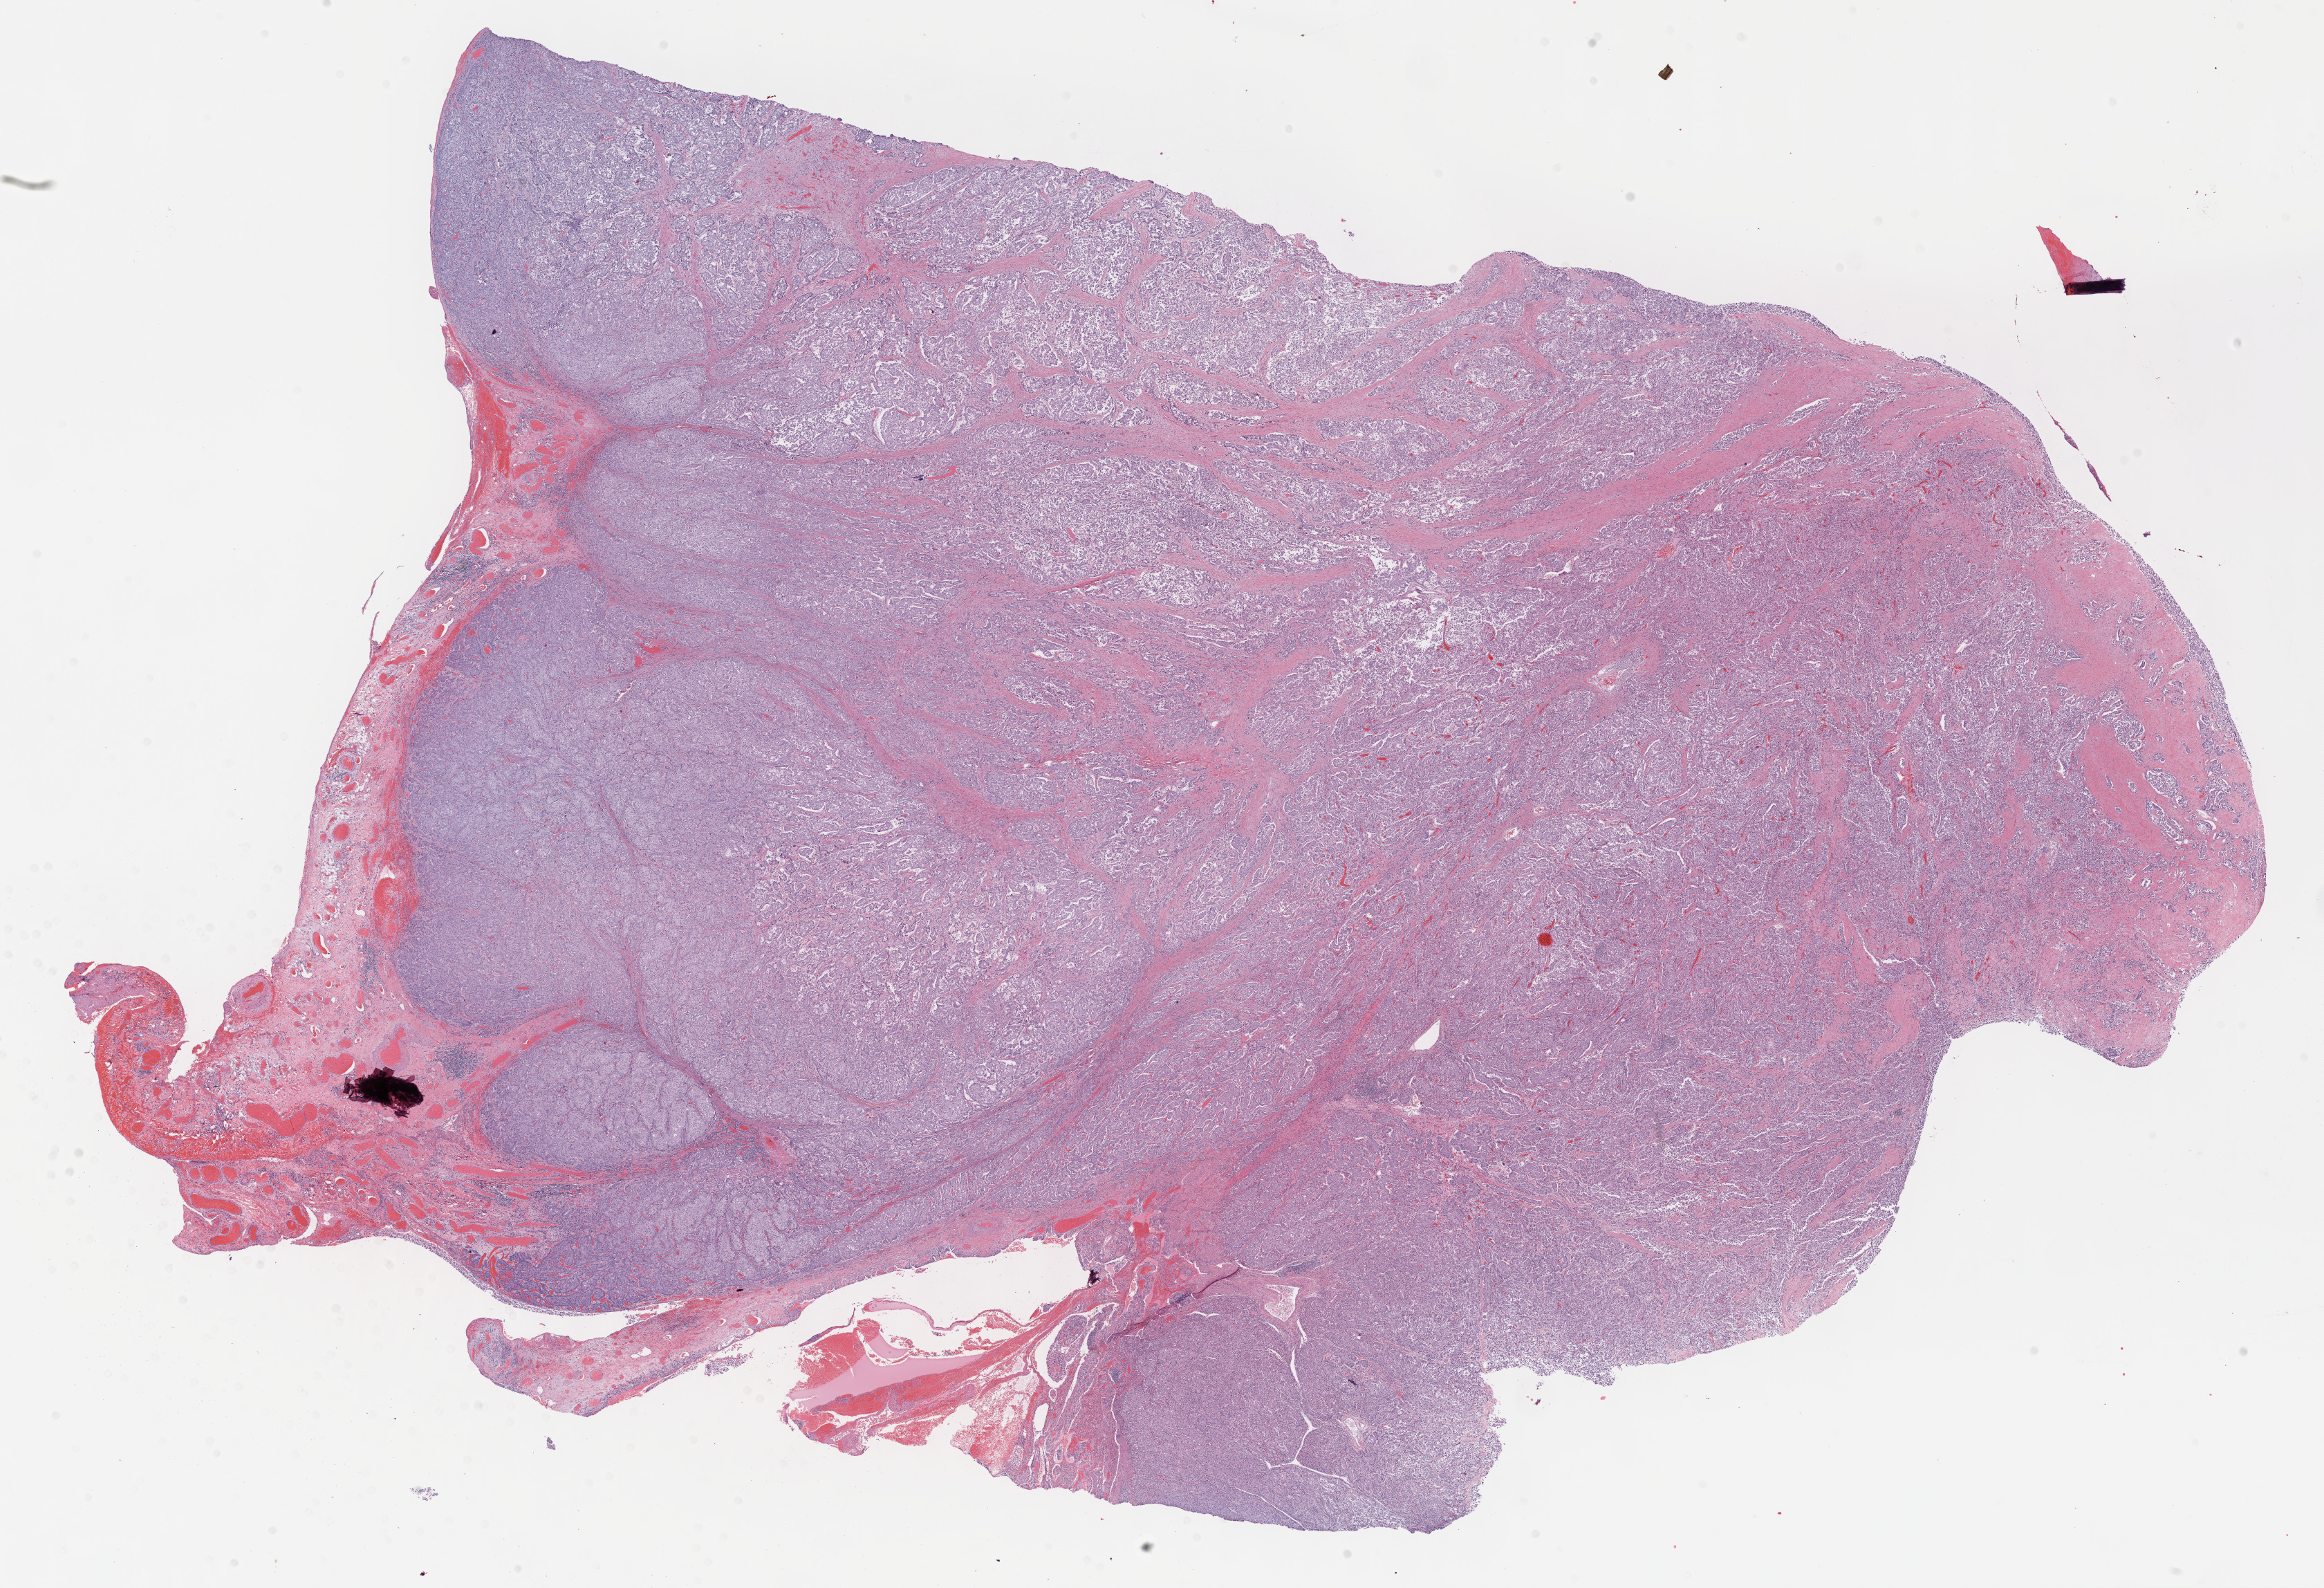
Whole-slide histology image, H&E — shown as a low-resolution overview of the whole scanned area (about 27.2 x 18.6 mm). Formalin-fixed paraffin-embedded (FFPE) diagnostic section. Primary tumour sample from the lung. Patient: male, age at initial diagnosis 41 years.
Pathologic diagnosis: Mucinous adenocarcinoma (upper lobe, lung).